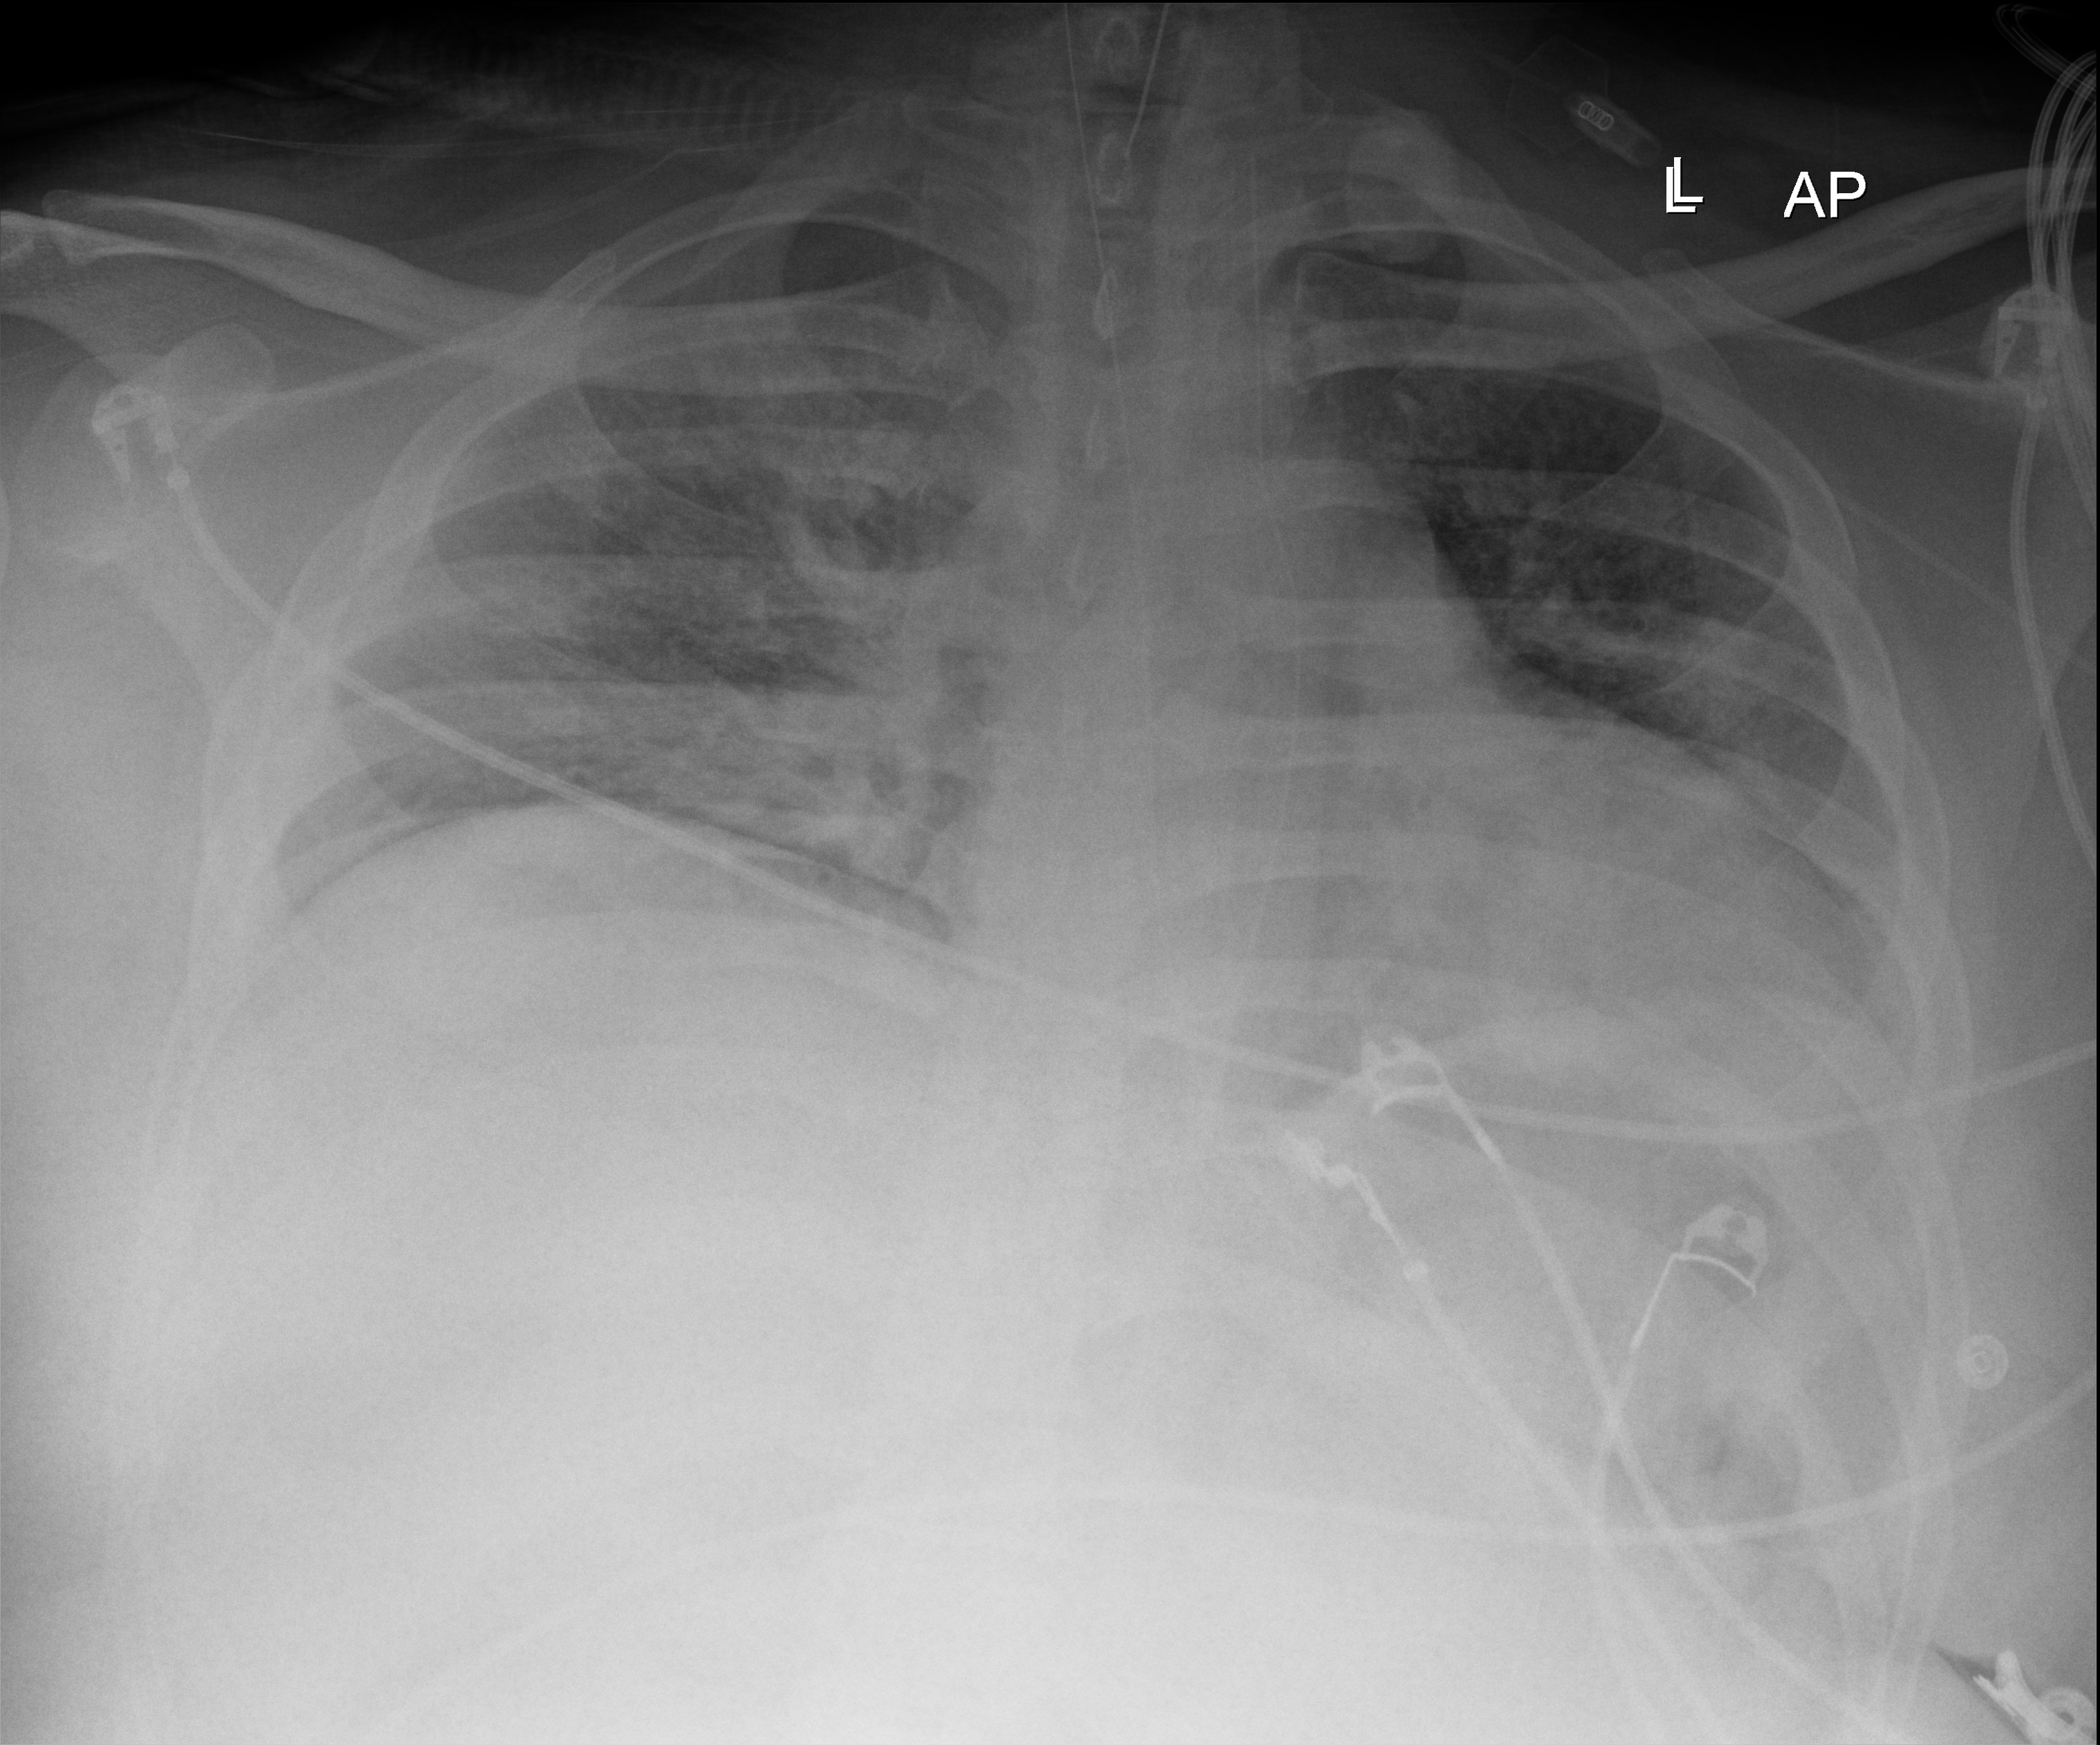
Chest X-ray (portable); anteroposterior (AP) projection. Male patient hospitalised with COVID-19, age 18–59 years.
Hospital-stay facts (about this admission, not read from this image; timing relative to this image not recorded): mechanically ventilated during this hospital stay: yes.